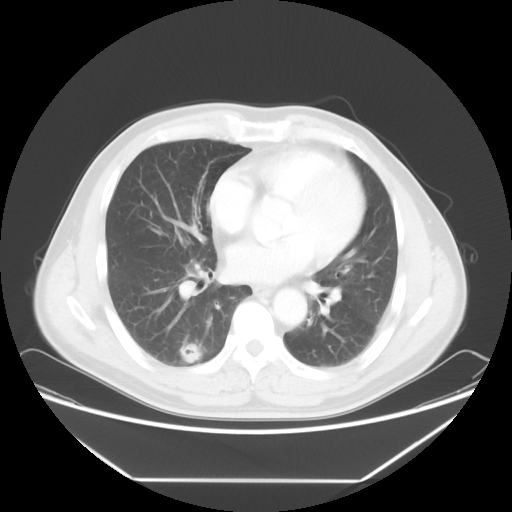
Chest CT, one axial slice. Slice 32 of 65 in the series (ordered by position). Lung window (W 1500 / L -600 HU). 512 × 512 image matrix, field of view 418 × 418 mm. Male patient, age 50 years. Case-level facts recorded for this patient, not image findings: clinical TNM (as recorded): T1c N0 M0; histopathological grade: G3.
Outlined on this slice (bounding box drawn by a radiologist):
- lung tumour (recorded histology: adenocarcinoma): bounding box [x1, y1, x2, y2] px = [174, 337, 206, 366]